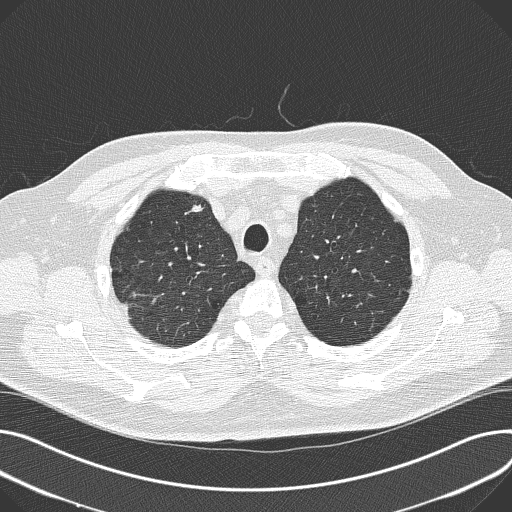
Axial slice from a low-dose chest CT screening exam. Third annual screen. Lung window (W 1500 / L -600 HU). 2 mm slice thickness. Male participant, aged 68 years at enrolment.
Expert reader's lesion annotation, bounding box (x1, y1, x2, y2) in pixels: (178, 188, 218, 227). The screening reader recorded 3 non-calcified nodules or masses ≥4 mm on this exam (right upper lobe, left lower lobe, right lower lobe); which of them this box marks is not recorded. Participant outcome: lung cancer diagnosed 95 days after this screen — combined small cell carcinoma, right upper lobe, undifferentiated (G4), stage IIIB (AJCC 6th edition), 30 mm at pathology.